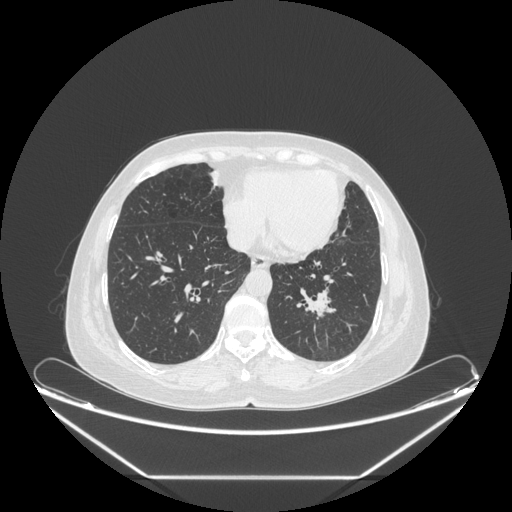
Chest CT, one axial slice; slice 83 of 241 in the series (ordered by position); lung window (W 1500 / L -600 HU); 1.25 mm slice thickness; 512 × 512 image matrix, field of view 451 × 451 mm. Patient: female, 63 years. Case-level facts recorded for this patient, not image findings: clinical TNM (as recorded): T1c N0 M0; histopathological grade: G2-3.
Structures marked on this image (rectangle marked by the reading radiologist):
- lung tumour (recorded histology: adenocarcinoma): bounding box <304,281,337,335> (left, top, right, bottom; pixels)